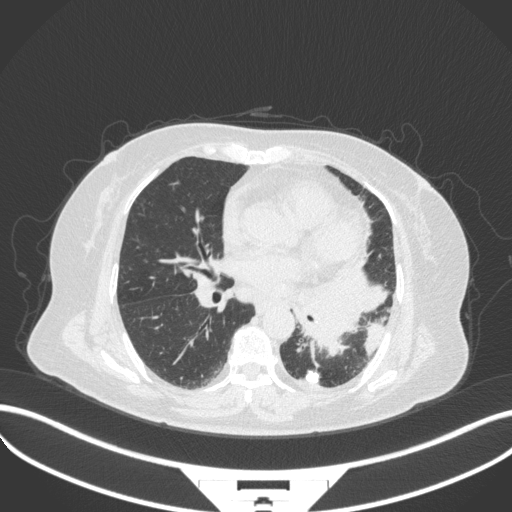
Chest CT, one axial slice. Slice 167 of 328 in the series (ordered by position). Reconstruction kernel B31f. Lung window (W 1500 / L -600 HU). 1 mm slice thickness. 512 × 512 image matrix. Patient: female, 69 years. Case-level facts recorded for this patient, not image findings: clinical TNM (as recorded): T2b N3 M1.
Annotated regions visible in this slice (rectangle marked by the reading radiologist):
- lung tumour (recorded histology: adenocarcinoma): bounding box <295,269,394,357> (left, top, right, bottom; pixels)